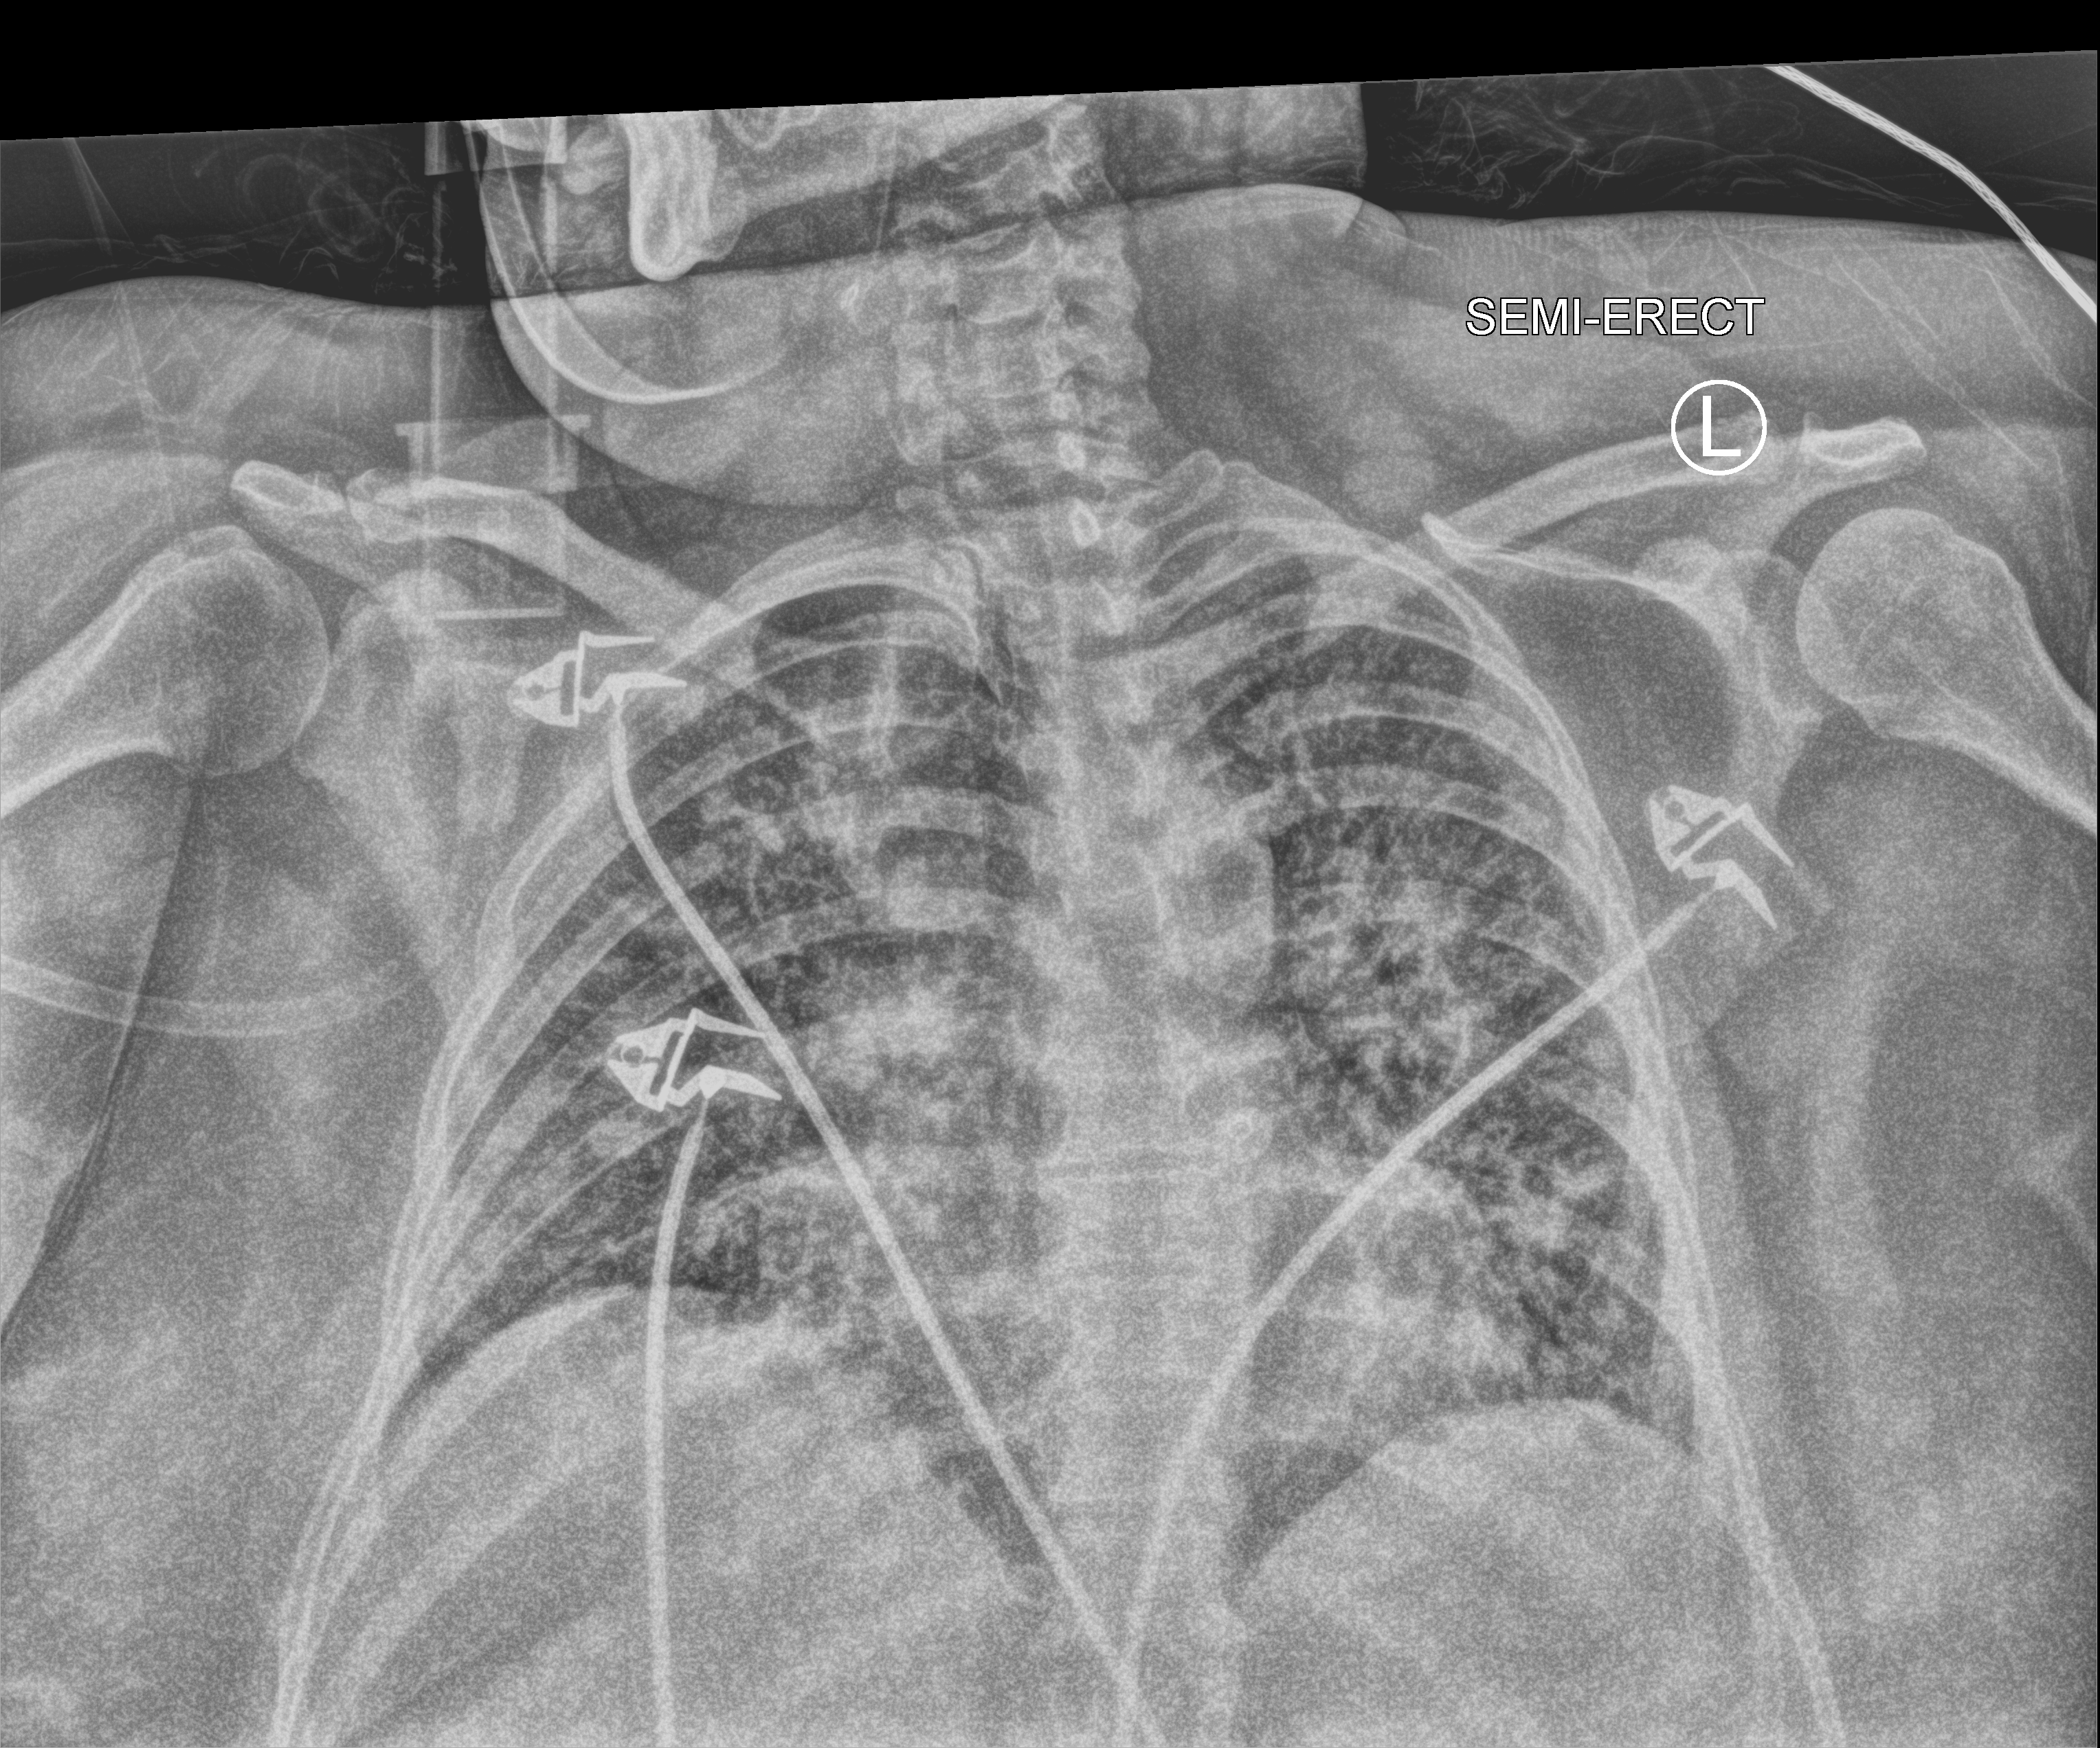
Chest X-ray (portable); anteroposterior (AP) projection. Patient hospitalised with COVID-19; female, aged 18–59 years.
Admission-level facts for this patient (not findings on this image; timing relative to this image not recorded):
- smoking status (admission record): never
- mechanically ventilated during this hospital stay: yes